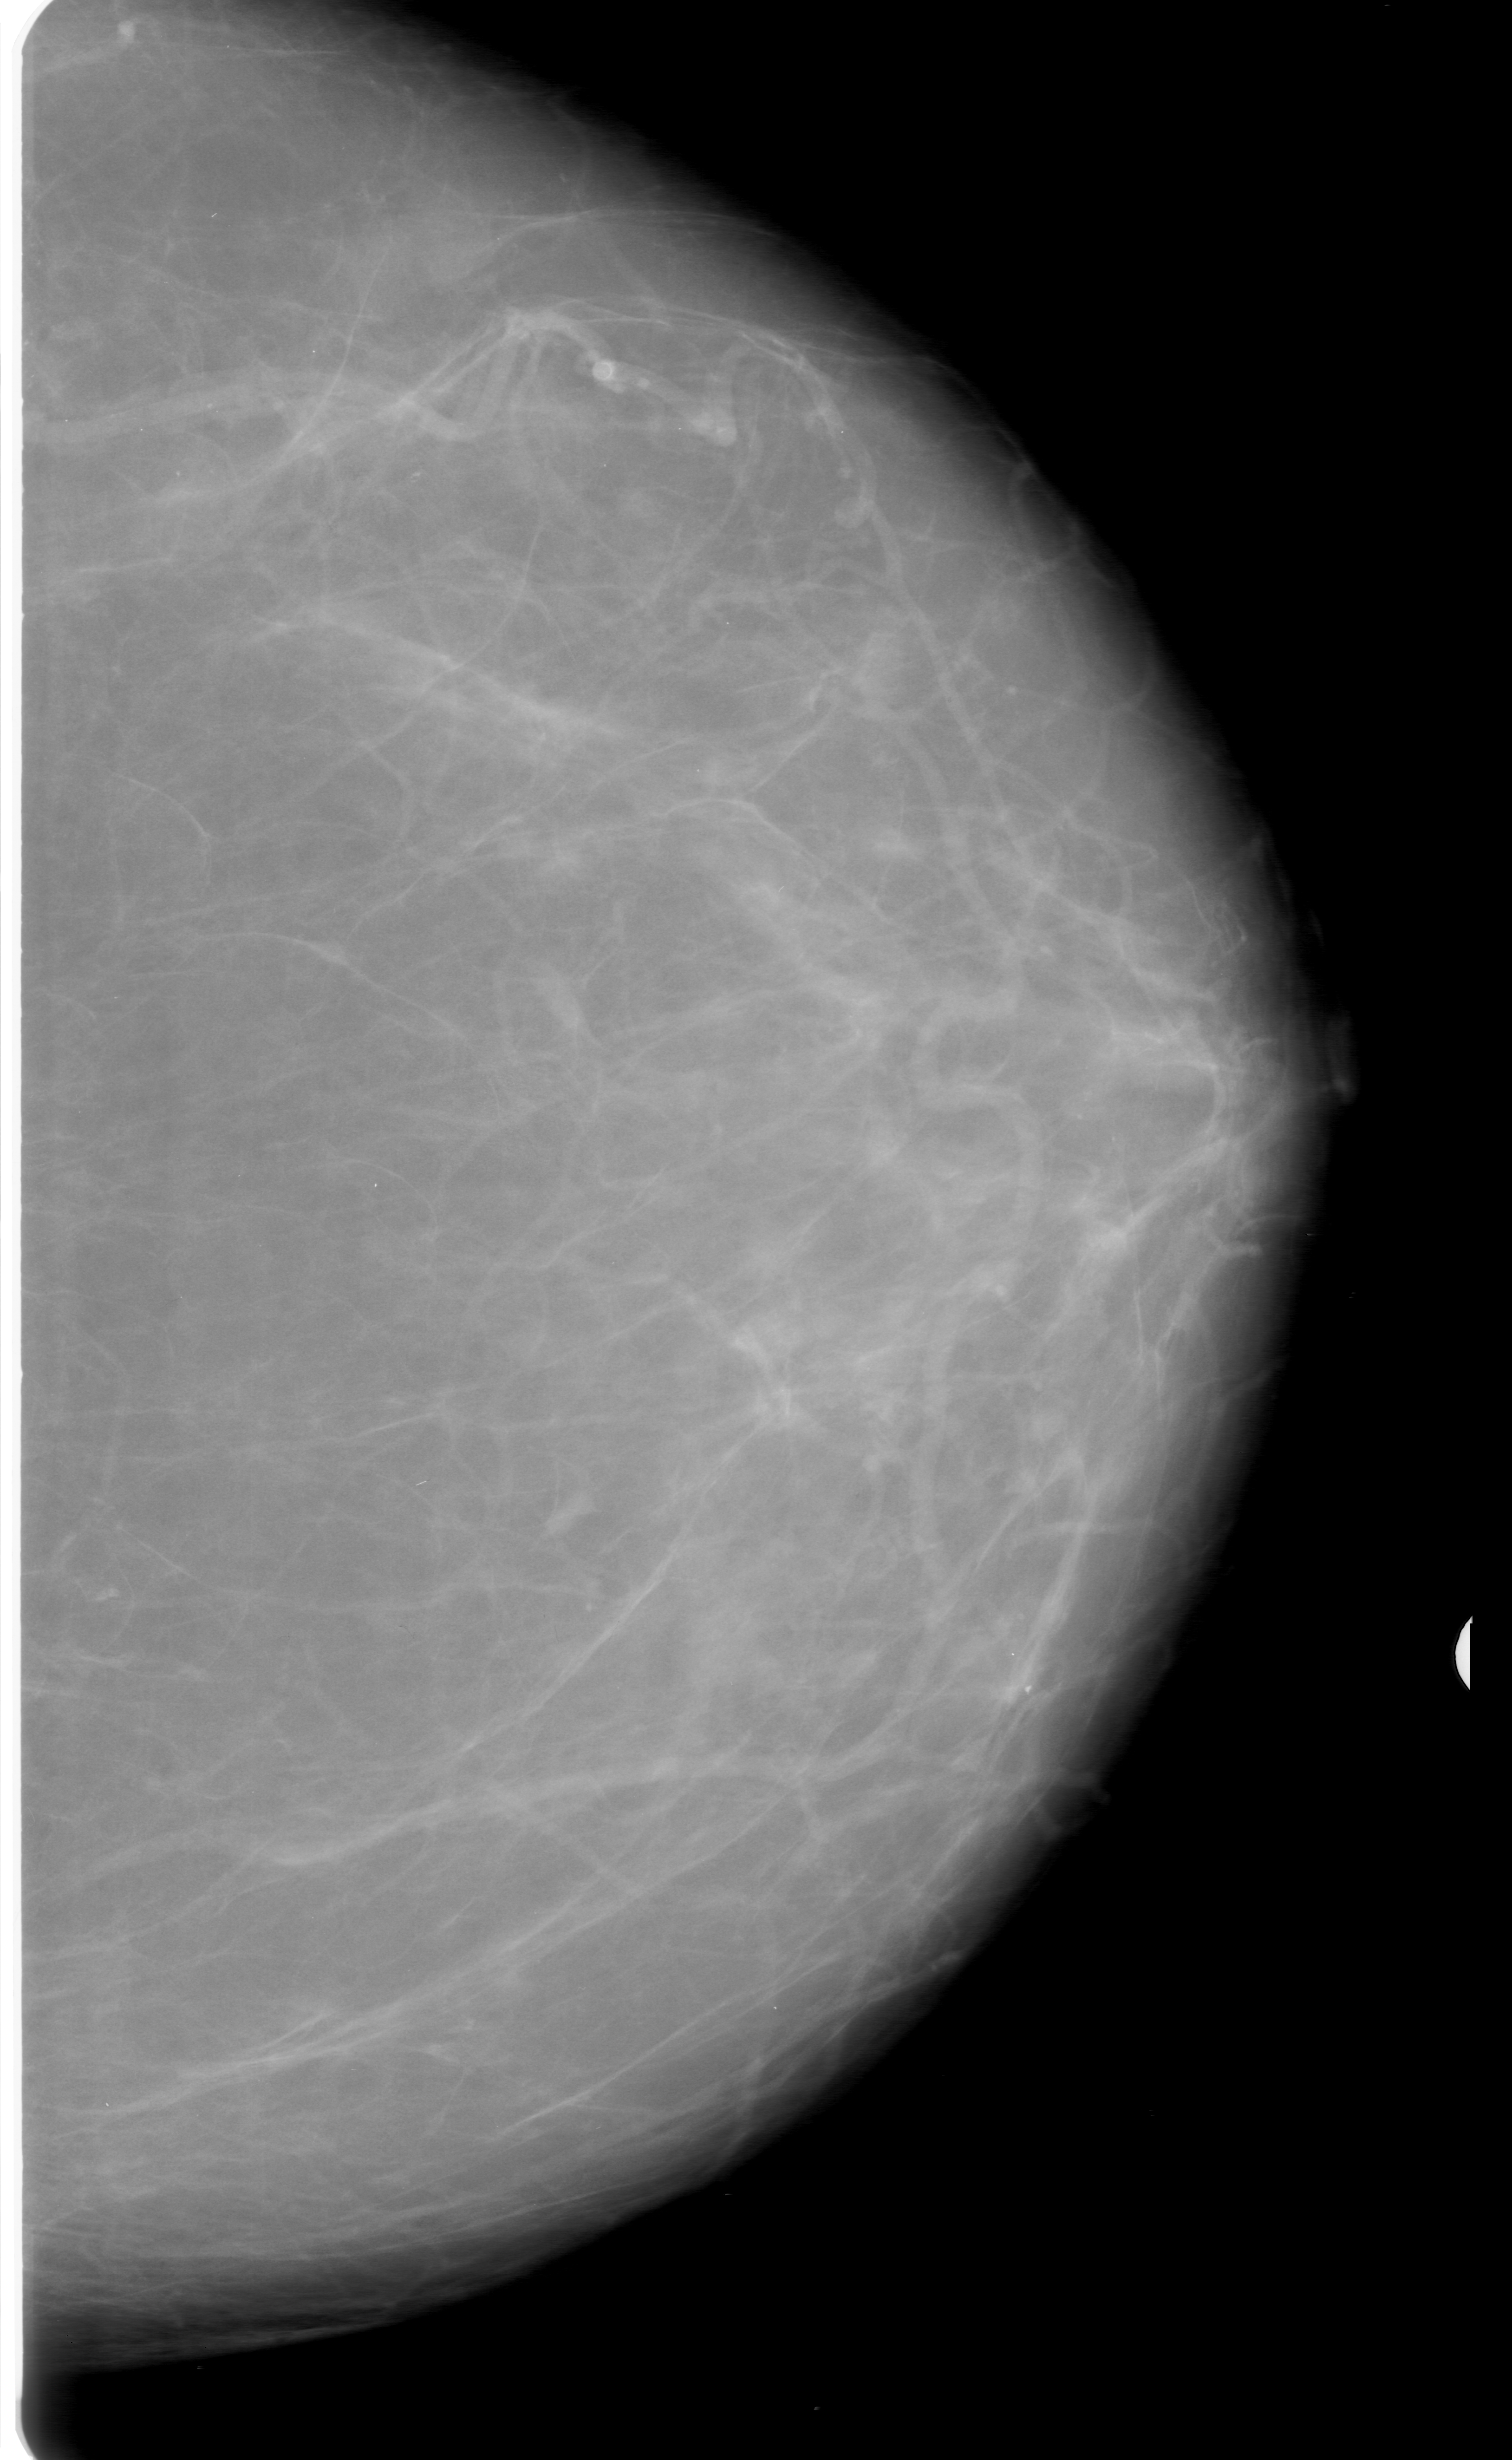
Scanned film-screen mammogram; left breast; craniocaudal (CC) view; BI-RADS breast density category 2 (scale 1–4).
Marked abnormality: calcifications, morphology amorphous, distribution linear; BI-RADS assessment category 3; subtlety rating 2 on a 1 (subtle) to 5 (obvious) scale; pathology (as recorded): malignant.